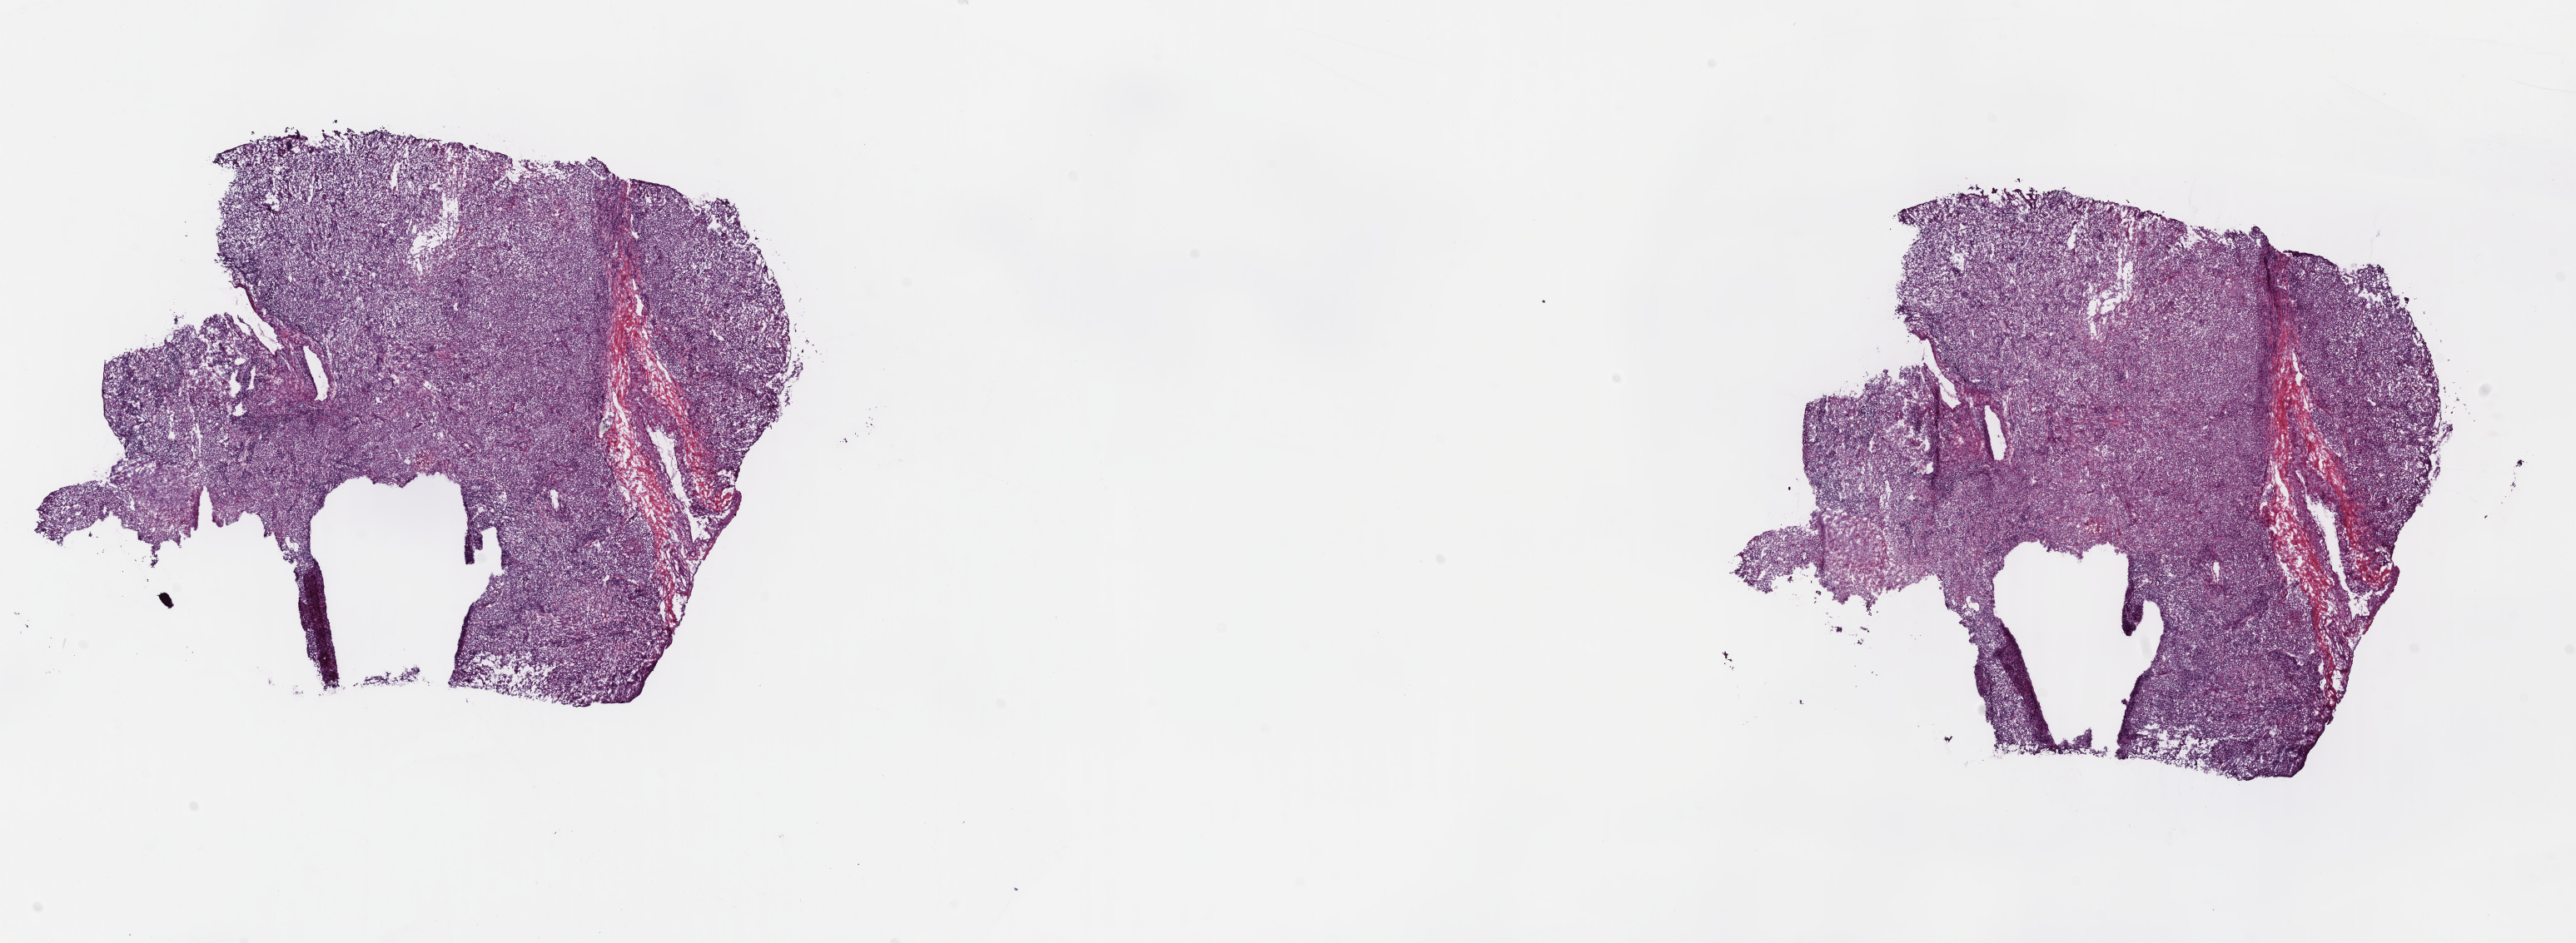
H&E whole-slide image — shown as a low-resolution overview of the whole scanned area (about 24.3 x 8.9 mm, acquisition: 40x scan), frozen section from the top of the tissue portion, sample: primary tumour, lung. Patient: female, age at initial diagnosis 78 years. Slide review estimates, as recorded: tumour cells 53%, tumour nuclei 60%.
Pathologic diagnosis: Squamous cell carcinoma, NOS (upper lobe, lung).